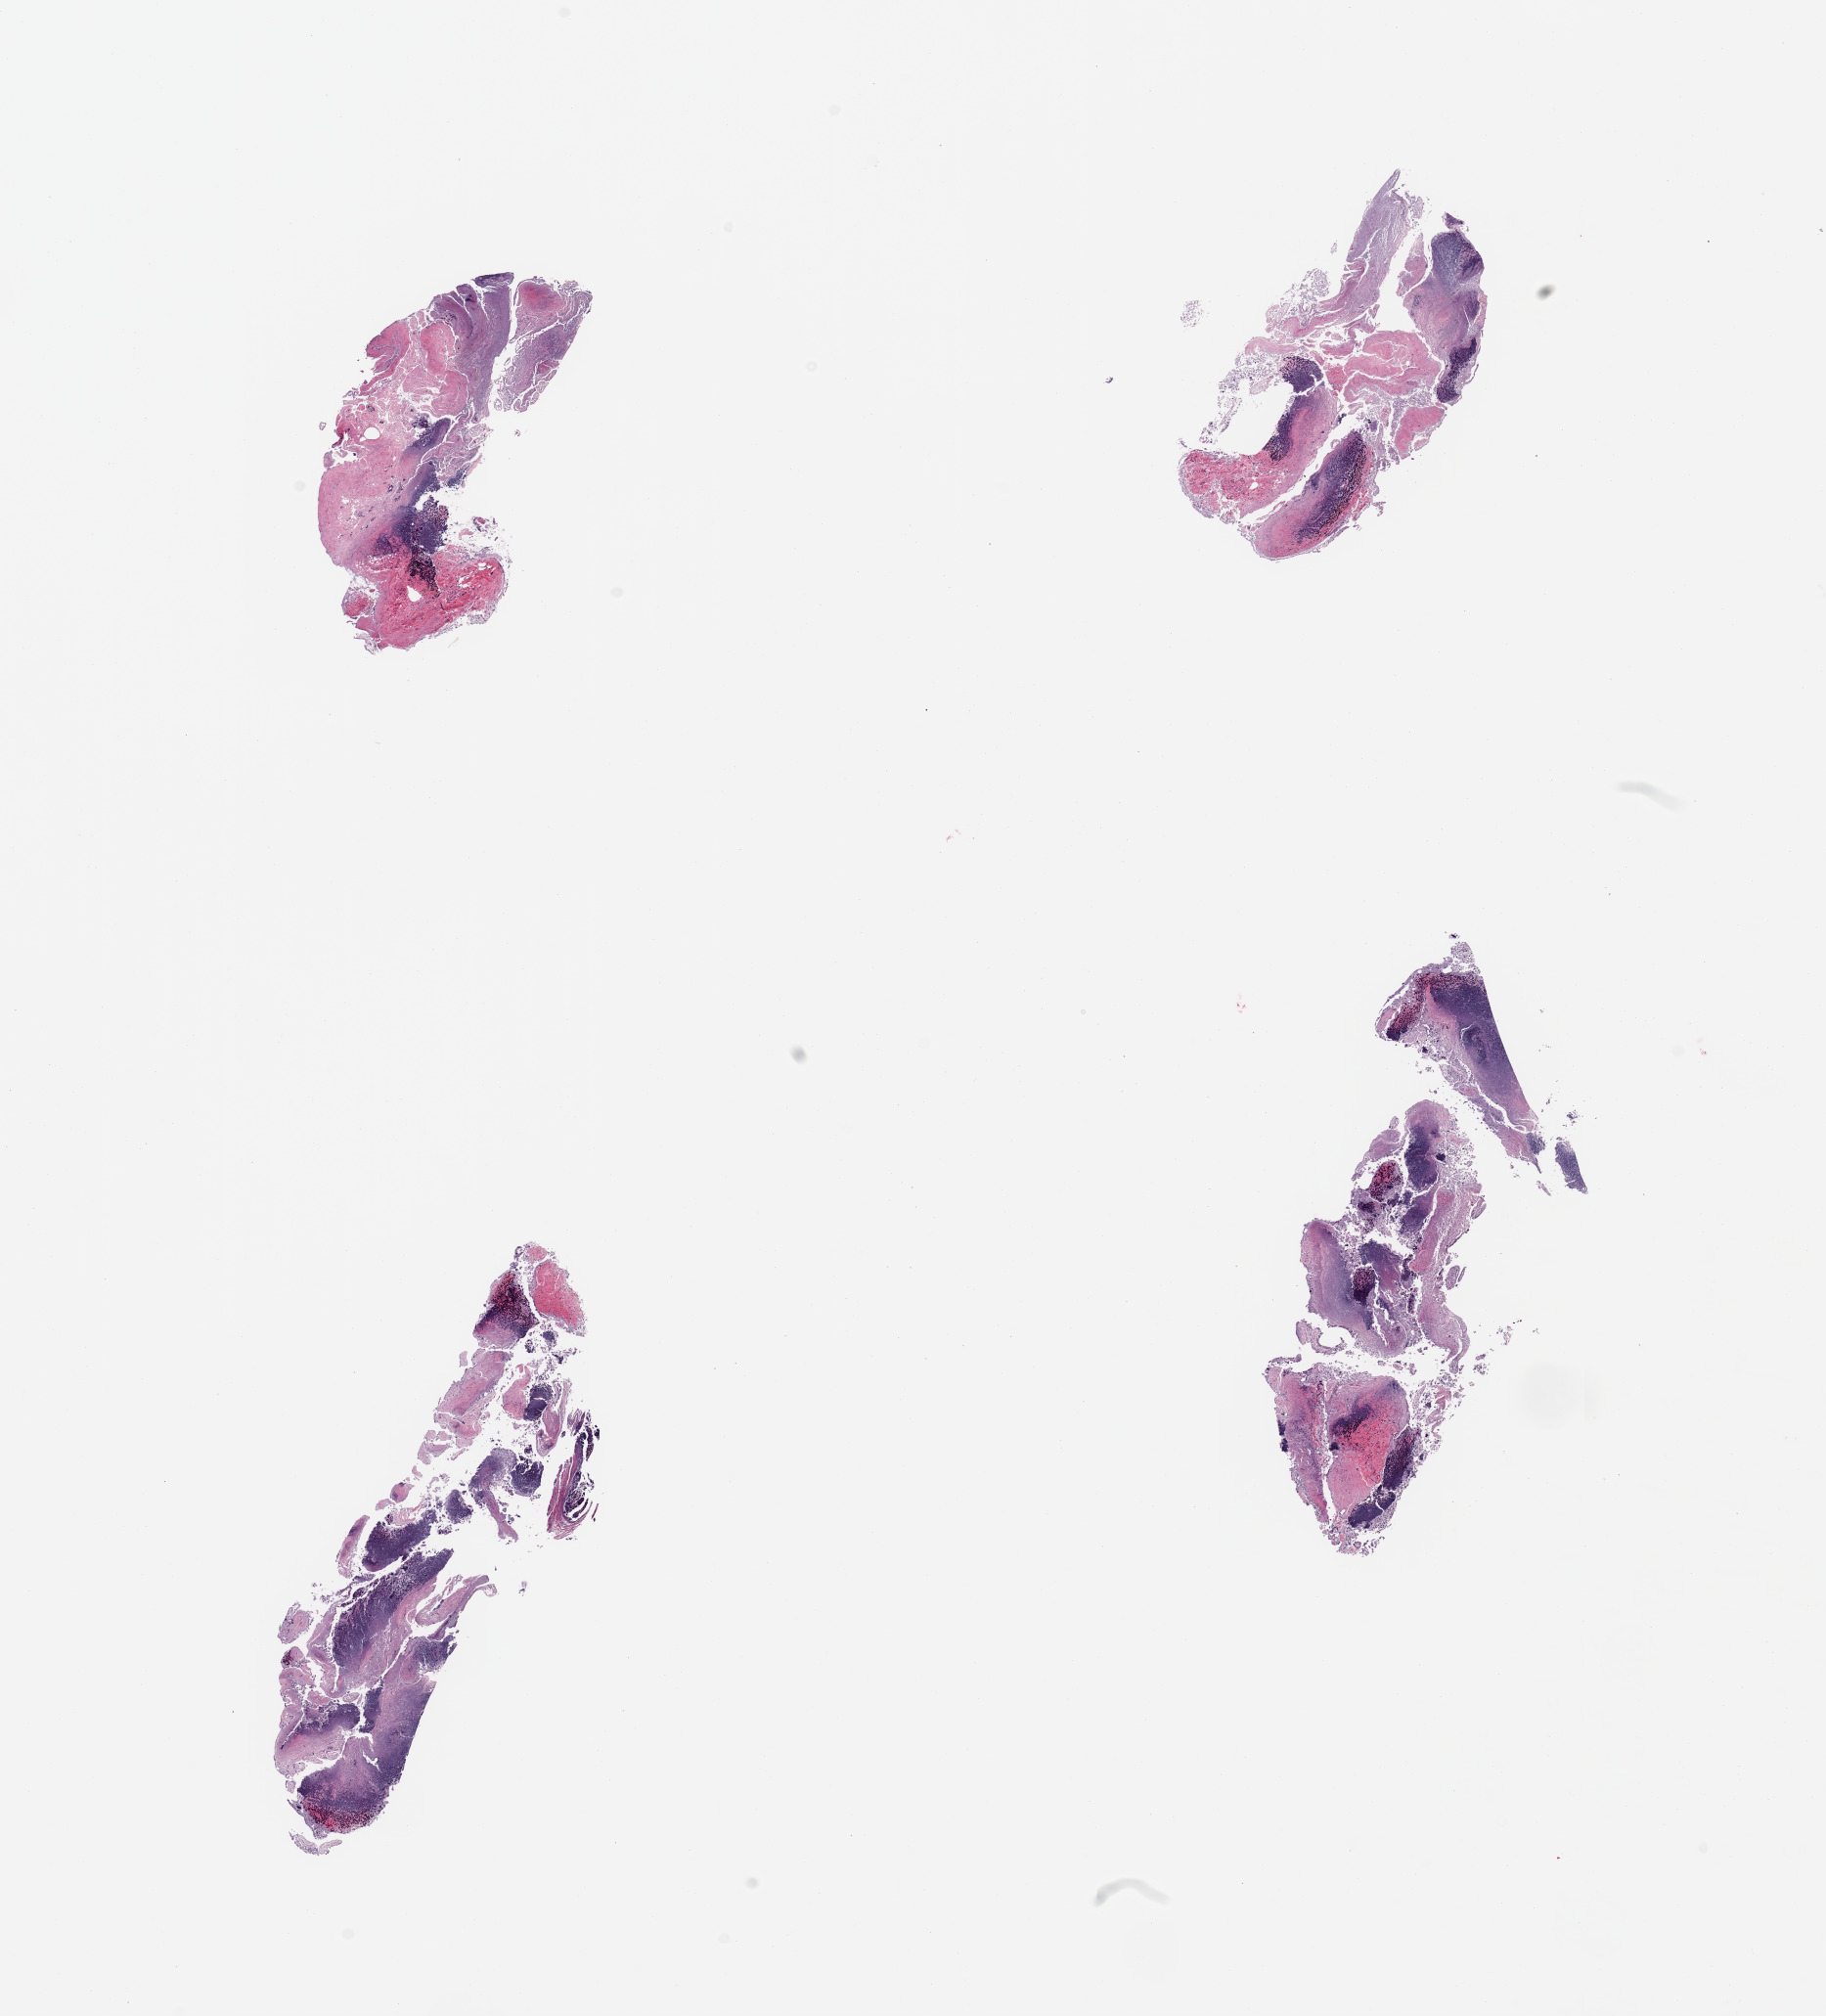
Whole-slide image, hematoxylin and eosin (H&E) stain — shown as a low-resolution overview of the whole scanned area (about 14.8 x 16.3 mm). PAXgene-fixed paraffin-embedded (PFPE) section. Sampled site (target tissue): ileum. Donor tissue sample. Female donor.
Review note (as recorded): 4 pieces; good lymphoid component, but too autolyzed.